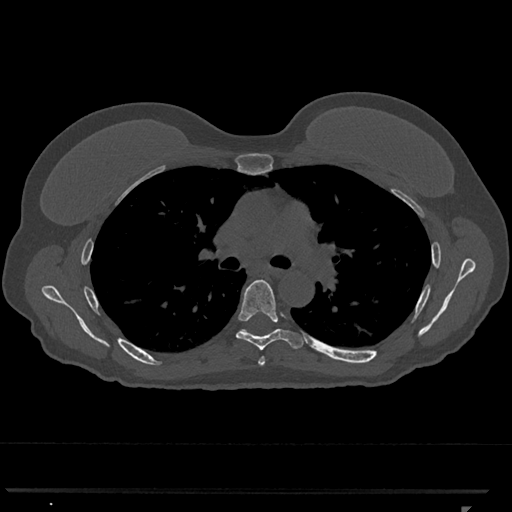
CT including the spine, one axial slice; position 761 of 793 along the scan axis; reconstruction kernel Br40s/3; 120 kVp; bone window (W 1800 / L 400 HU); 0.5 mm slice thickness; 512 × 512 image matrix, field of view 380 × 380 mm. Female patient, age 62 years. From the clinical record (not read from this slice): primary cancer: renal.
Structures marked on this image (semi-automatic segmentation, software-assisted and operator-edited):
- T5 vertebra: box from (x=258, y=357) to (x=265, y=366) px
- T6 vertebra: (x=236, y=279)–(x=303, y=351)